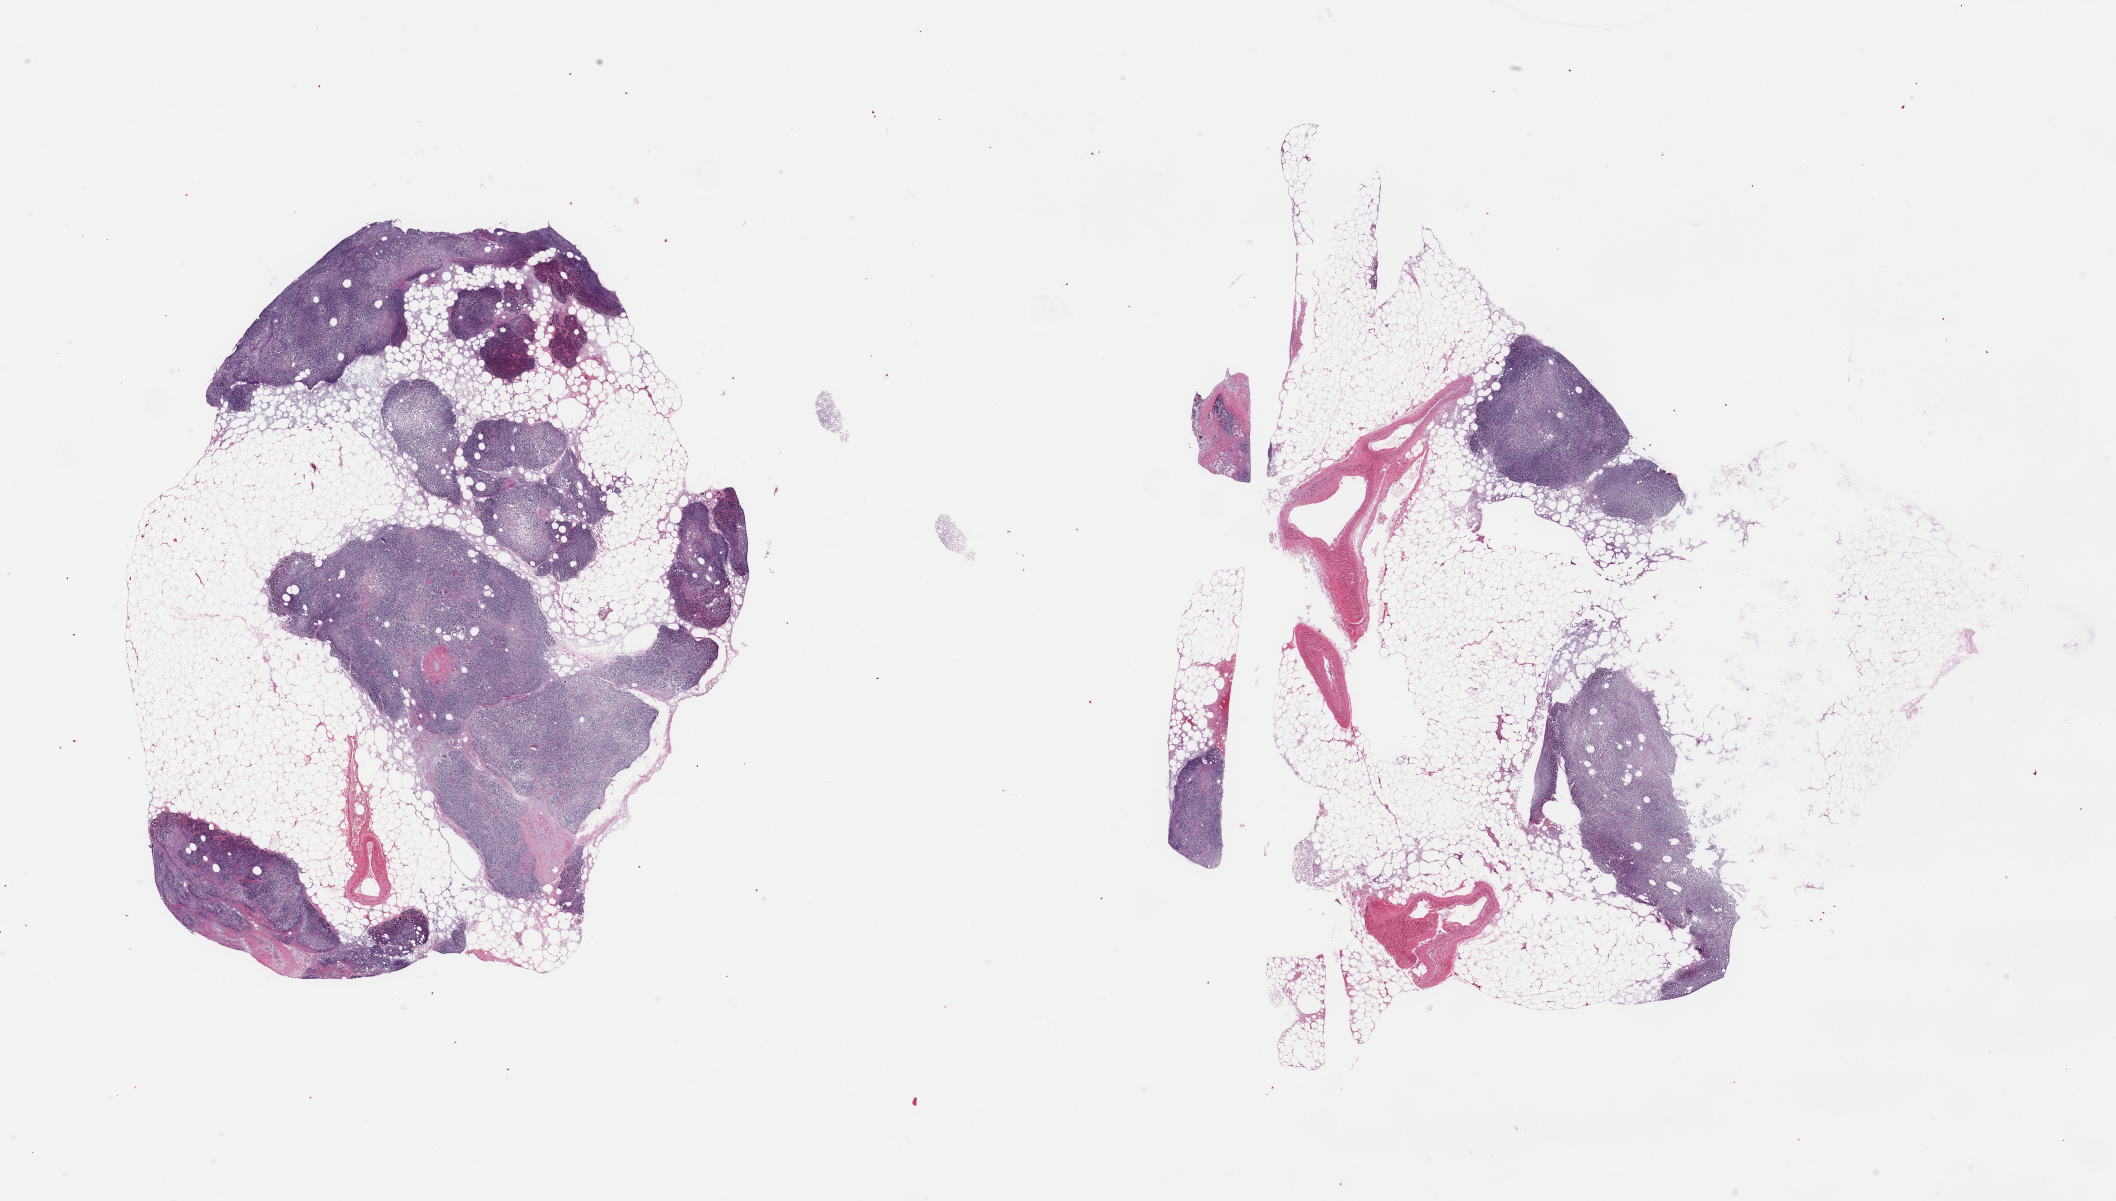
Whole-slide image, haematoxylin and eosin stain, a low-resolution overview of the entire scanned area, about 33.5 x 19.0 mm, PAXgene-fixed, paraffin-embedded tissue, sampled site (target tissue): pancreas, tissue donor sample. Male donor.
Pathologist's review note for this sample: 2 pieces, advanced saponification; no visible islets, ~40% fat.